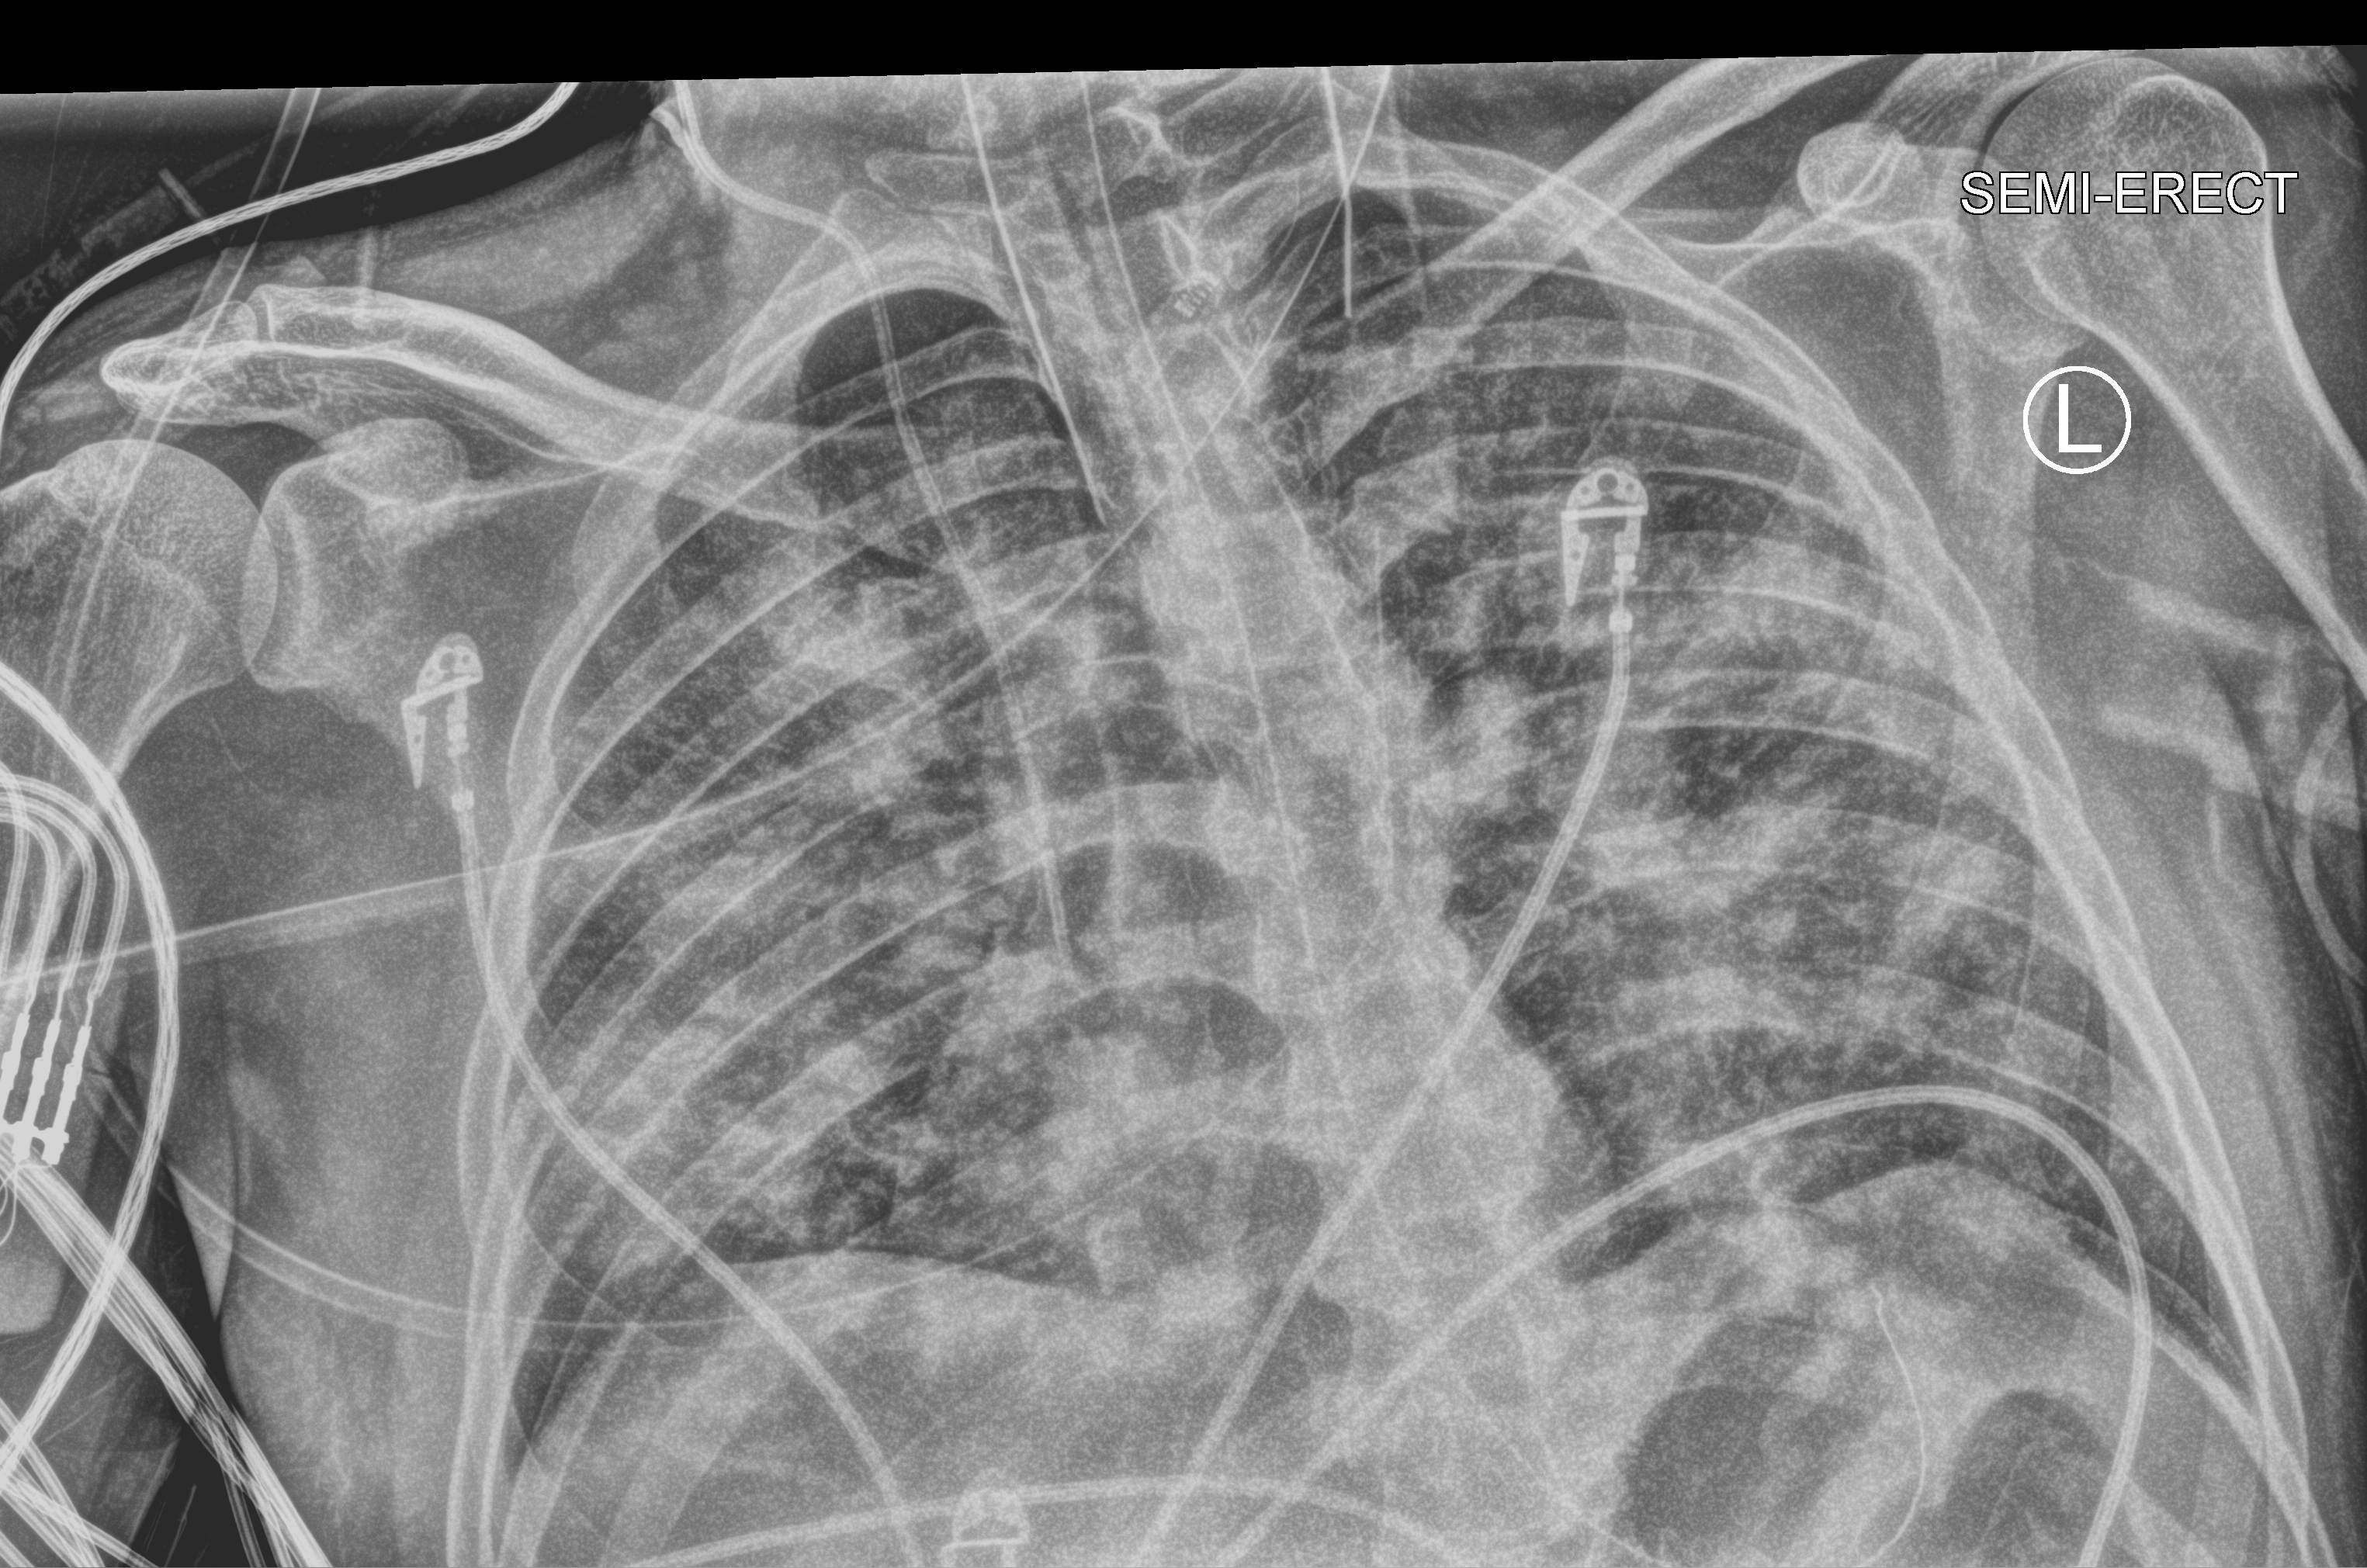
Portable chest radiograph; anteroposterior (AP) projection. Male patient hospitalised with COVID-19, age 18–59 years.
Admission-level facts for this patient (not findings on this image; timing relative to this image not recorded):
- admitted to intensive care during this hospital stay: yes